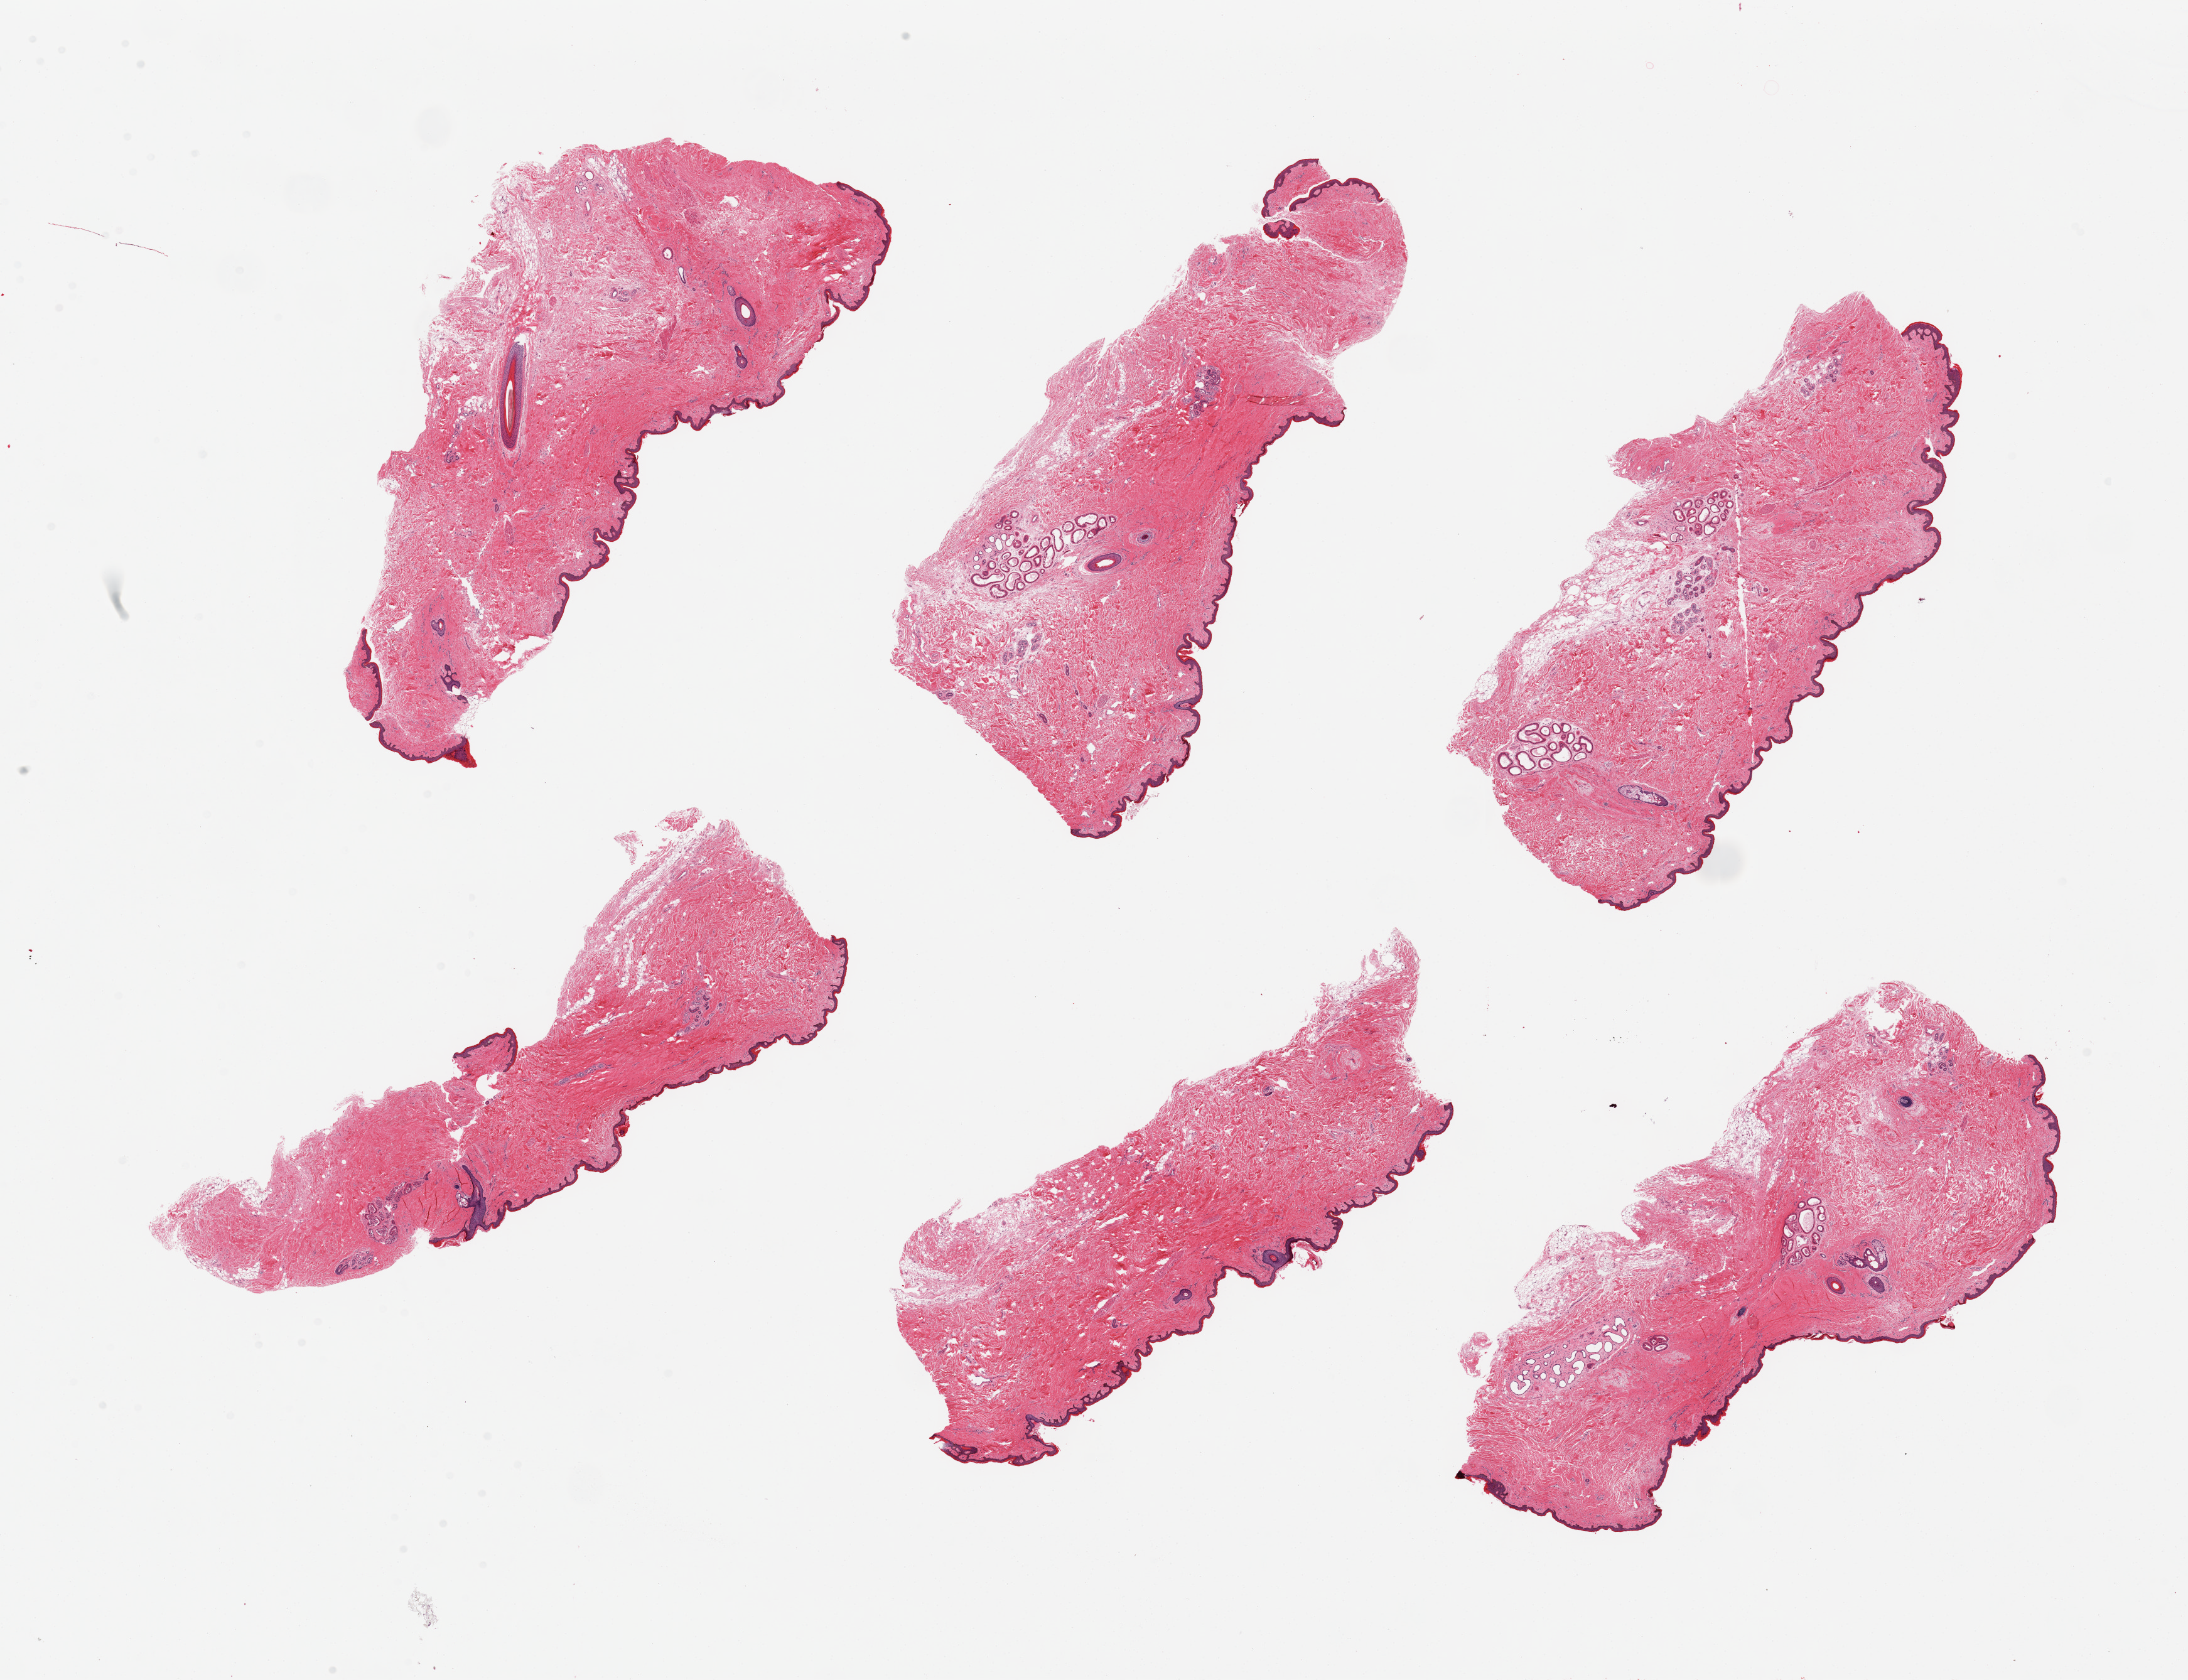
Digitized H&E-stained section, whole scanned area (about 27.6 x 21.2 mm) shown as a low-resolution overview, PAXgene-fixed, paraffin-embedded tissue, target tissue: skin of suprapubic region, tissue donor sample. Female donor.
Reviewer comment on this tissue sample: 6 pieces, no significant dermal fat; squamous epithelium is ~30 microns.